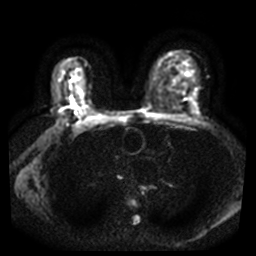
Breast MRI, one axial slice; position 24 of 44 along the scan axis; diffusion-weighted series; image 2 of 4 stored at this slice position (different b-values; order by instance number); 3 T; 5 mm slice thickness; 256 × 256 image matrix, field of view 340 × 340 mm. Female patient.
Annotated regions visible in this slice (outlined manually by an expert reader):
- tumour on diffusion-weighted imaging: bounding box (x1, y1, x2, y2) in pixels: (70, 99, 77, 109)